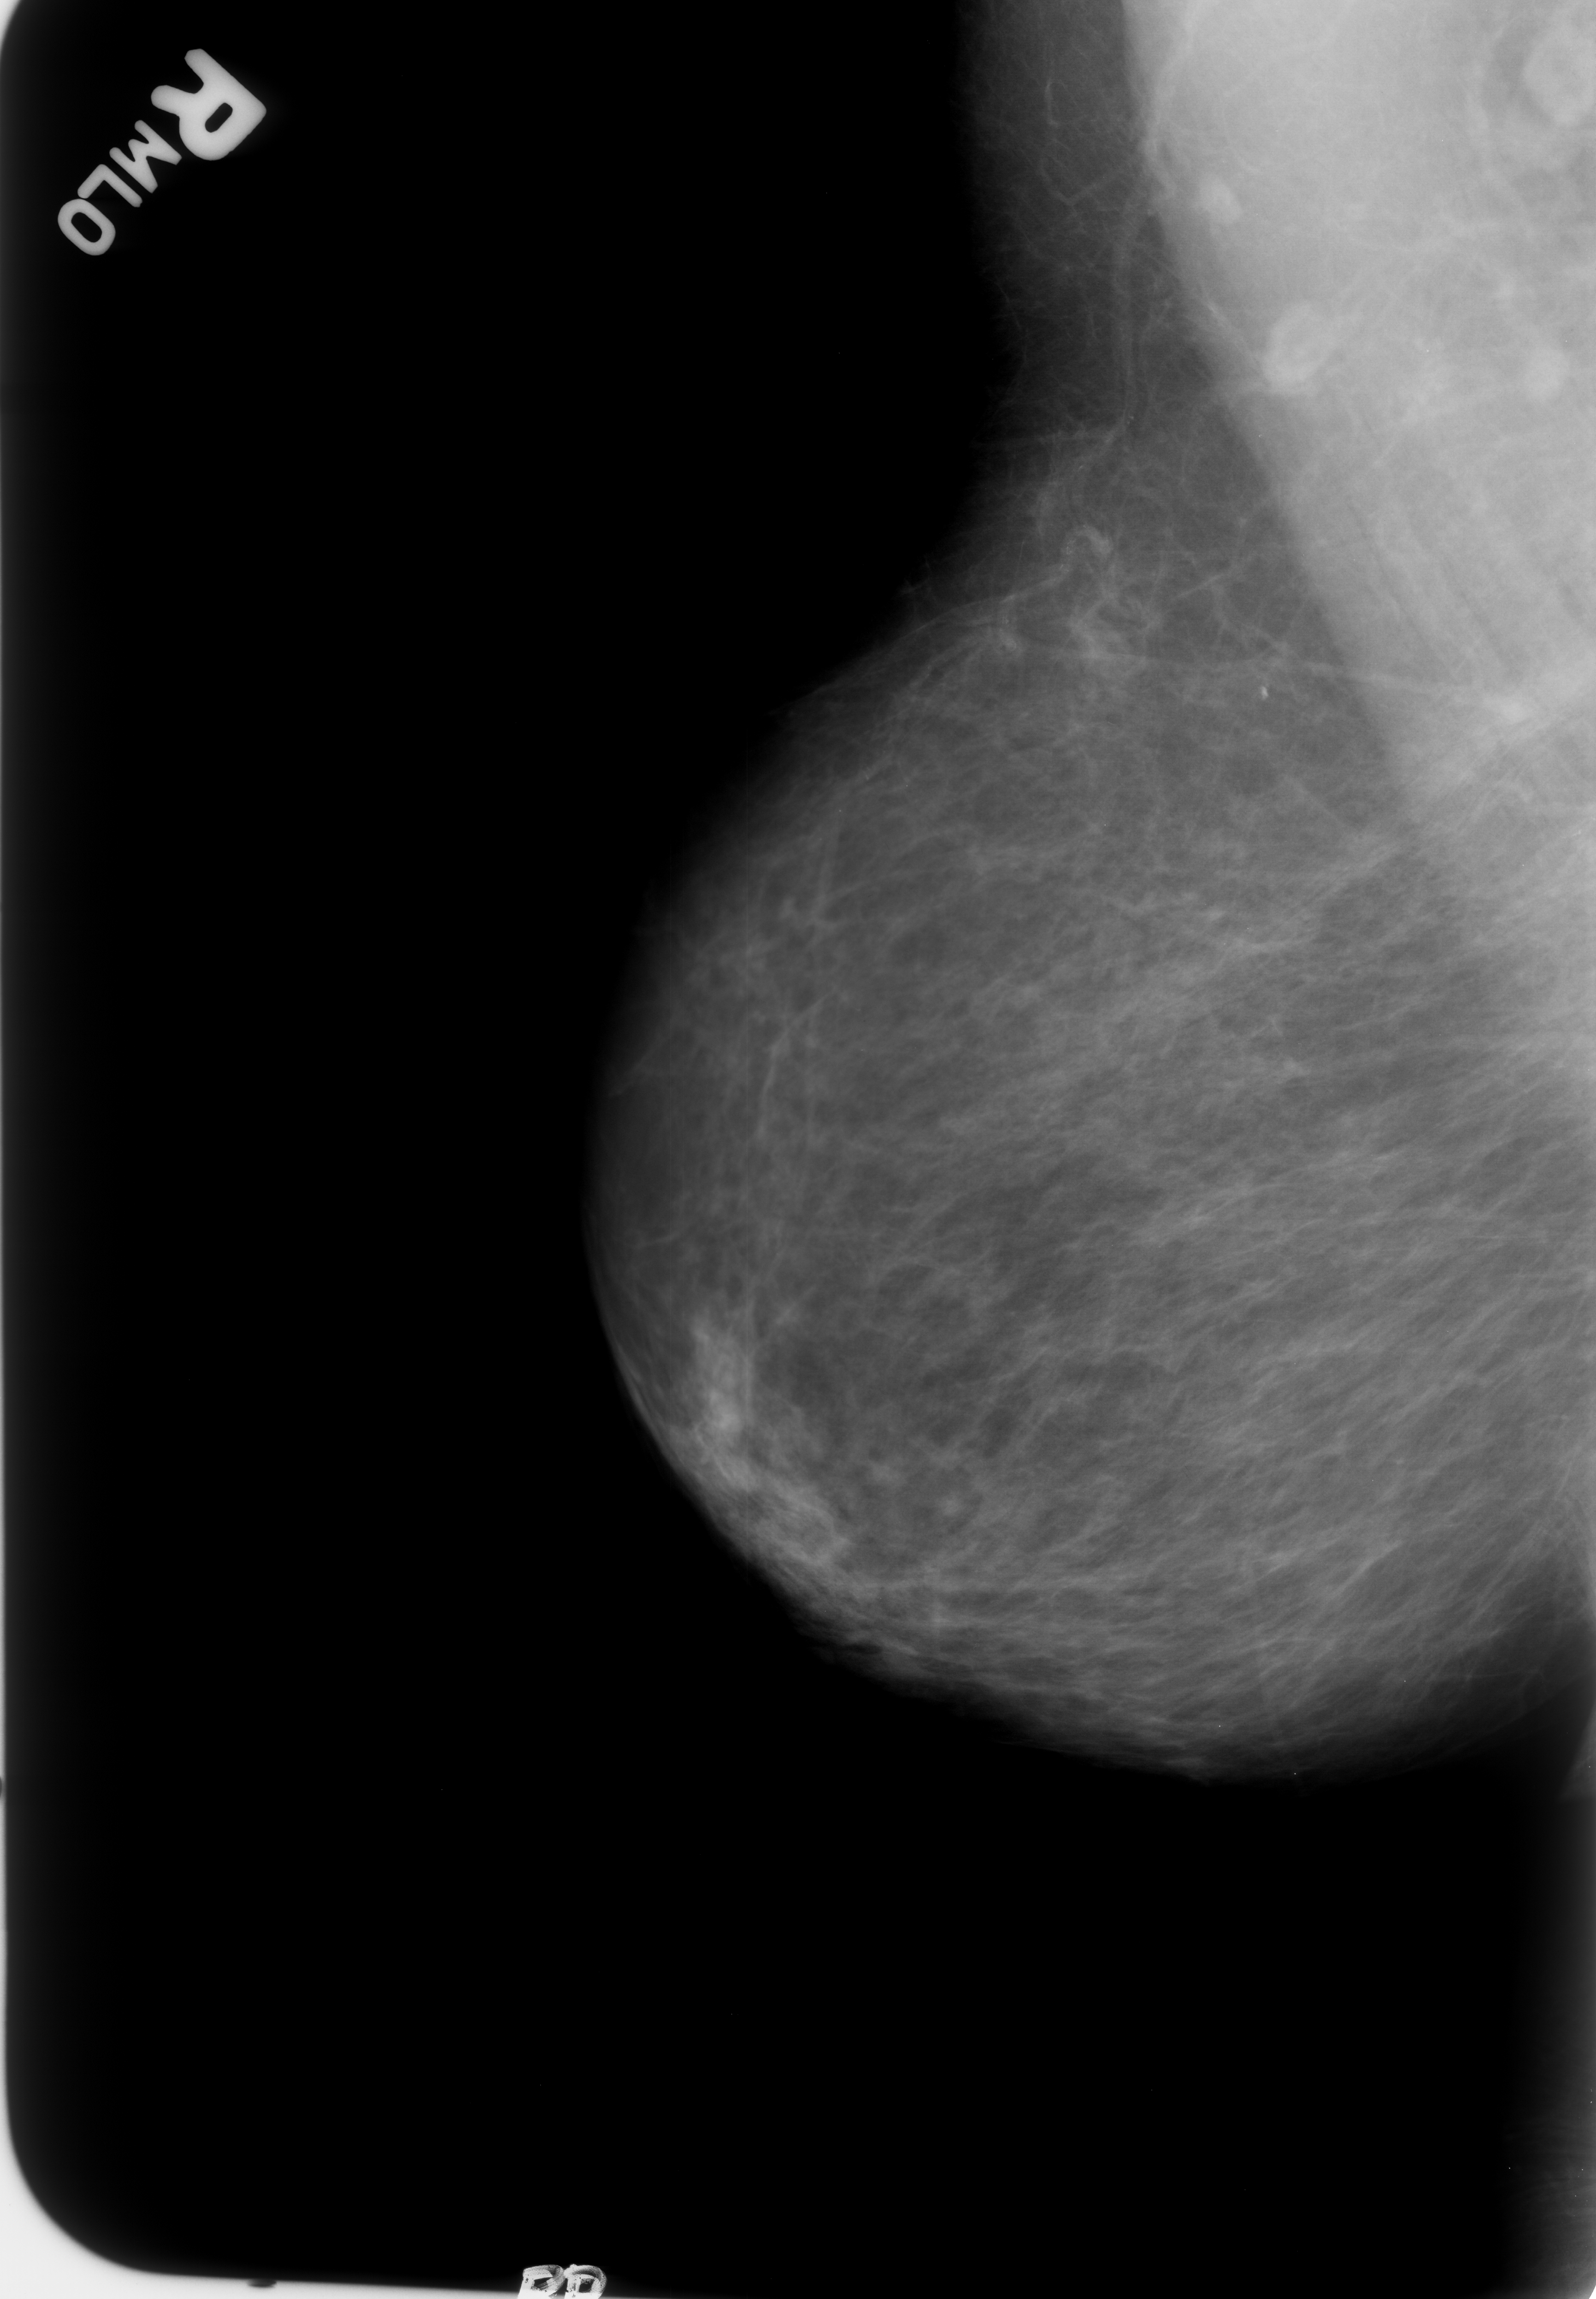
Digitized screen-film mammogram. Right breast. Mediolateral oblique (MLO) view. 1596 × 2299 image matrix.
Marked abnormalities (boxes around the expert regions of interest):
- calcifications, morphology coarse; BI-RADS assessment category 2; subtlety rating 4 on a 1 (subtle) to 5 (obvious) scale; benign; no additional work-up was recommended (outcome (as recorded, no biopsy): benign without callback): bounding box (x1, y1, x2, y2) in pixels: (1224, 660, 1298, 720)